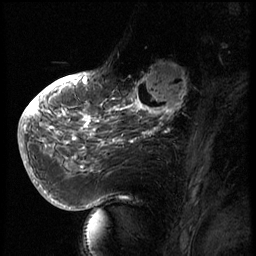
Breast MRI (dynamic contrast-enhanced), one sagittal slice. 3 images stored at this slice position (order not interpretable as contrast timing). 1.5 T. TE 4.2 ms, TR 8.9 ms. 2.5 mm slice thickness. 256 × 256 image matrix, field of view 200 × 200 mm. Female patient, age 56 years. From the clinical record (not read from this slice): setting: breast cancer imaged before/during neoadjuvant chemotherapy.
Outlined on this slice (semi-automatic segmentation, software-assisted and operator-edited):
- analysis volume of interest (the breast-tissue region the enhancement analysis was run in; not a lesion): bounding box (x1, y1, x2, y2) in pixels: (129, 62, 194, 127)
- tumour enhancement mask (voxels above the 140 % enhancement threshold inside the analysis volume of interest): (129, 65, 188, 127)